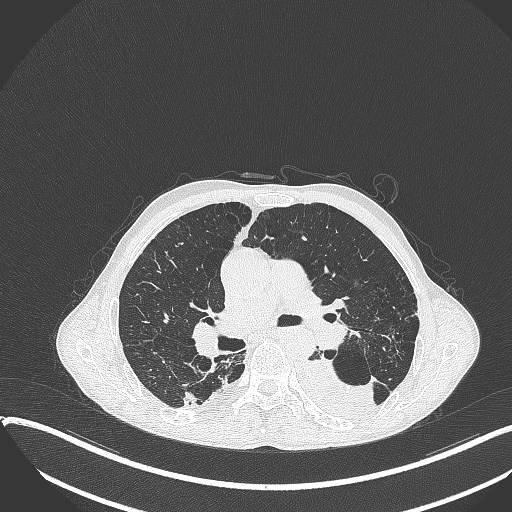
Chest CT, one axial slice; slice 228 of 401 in the series (ordered by position); 120 kVp; lung window (W 1500 / L -600 HU); 512 × 512 image matrix. Male patient, age 57 years. From the clinical record (not read from this slice): clinical TNM (as recorded): T4 N0 M0.
Annotated regions visible in this slice (rectangle marked by the reading radiologist):
- lung tumour (recorded histology: squamous cell carcinoma): bounding box [x1, y1, x2, y2] px = [297, 354, 383, 426]